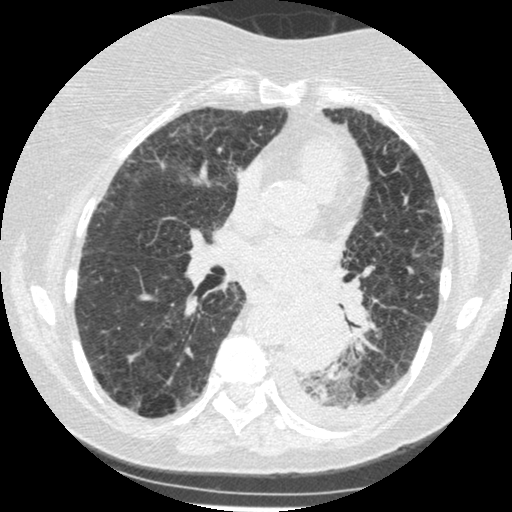
Low-dose screening chest CT, one axial slice. Position 124 of 341 along the scan axis. Reconstruction kernel STANDARD. 120 kVp. Lung window (W 1500 / L -600 HU). 1.25 mm slice thickness. 512 × 512 image matrix, field of view 310 × 310 mm.
Annotated regions visible in this slice (outlined manually by an expert reader):
- lesion 1 (tumor, lower lobe of left lung): box from (x=284, y=302) to (x=345, y=374) px